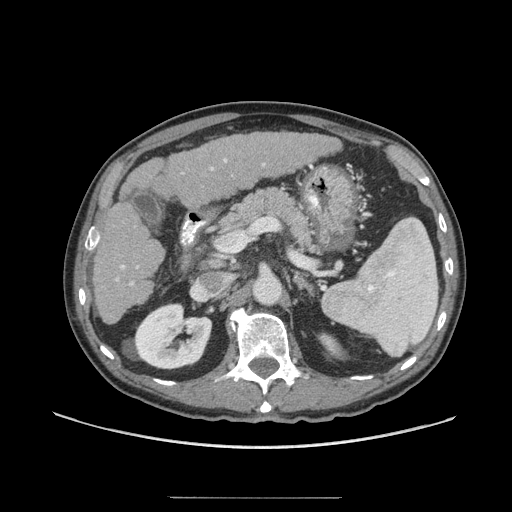
Contrast-enhanced abdominal CT (liver protocol), one axial slice. Slice 32 of 71 in the series (ordered by position). Reconstruction kernel STANDARD. Soft-tissue window (W 400 / L 40 HU). 512 × 512 image matrix, field of view 400 × 400 mm. From the clinical record (not read from this slice): diagnosis: hepatocellular carcinoma (patient treated with transarterial chemoembolisation; whether this scan precedes or follows treatment is not stated here); TNM stage (as recorded): Stage-I; Child-Pugh class: A; tumour differentiation: well differentiated; tumour nodularity: uninodular.
Structures marked on this image (semi-automatically segmented with operator editing):
- liver parenchyma outside the tumour (the mass and vessels are separate outlines, so this box may not span the whole liver): bounding box [x1, y1, x2, y2] px = [92, 132, 338, 324]
- liver vessels: [96, 158, 265, 285]